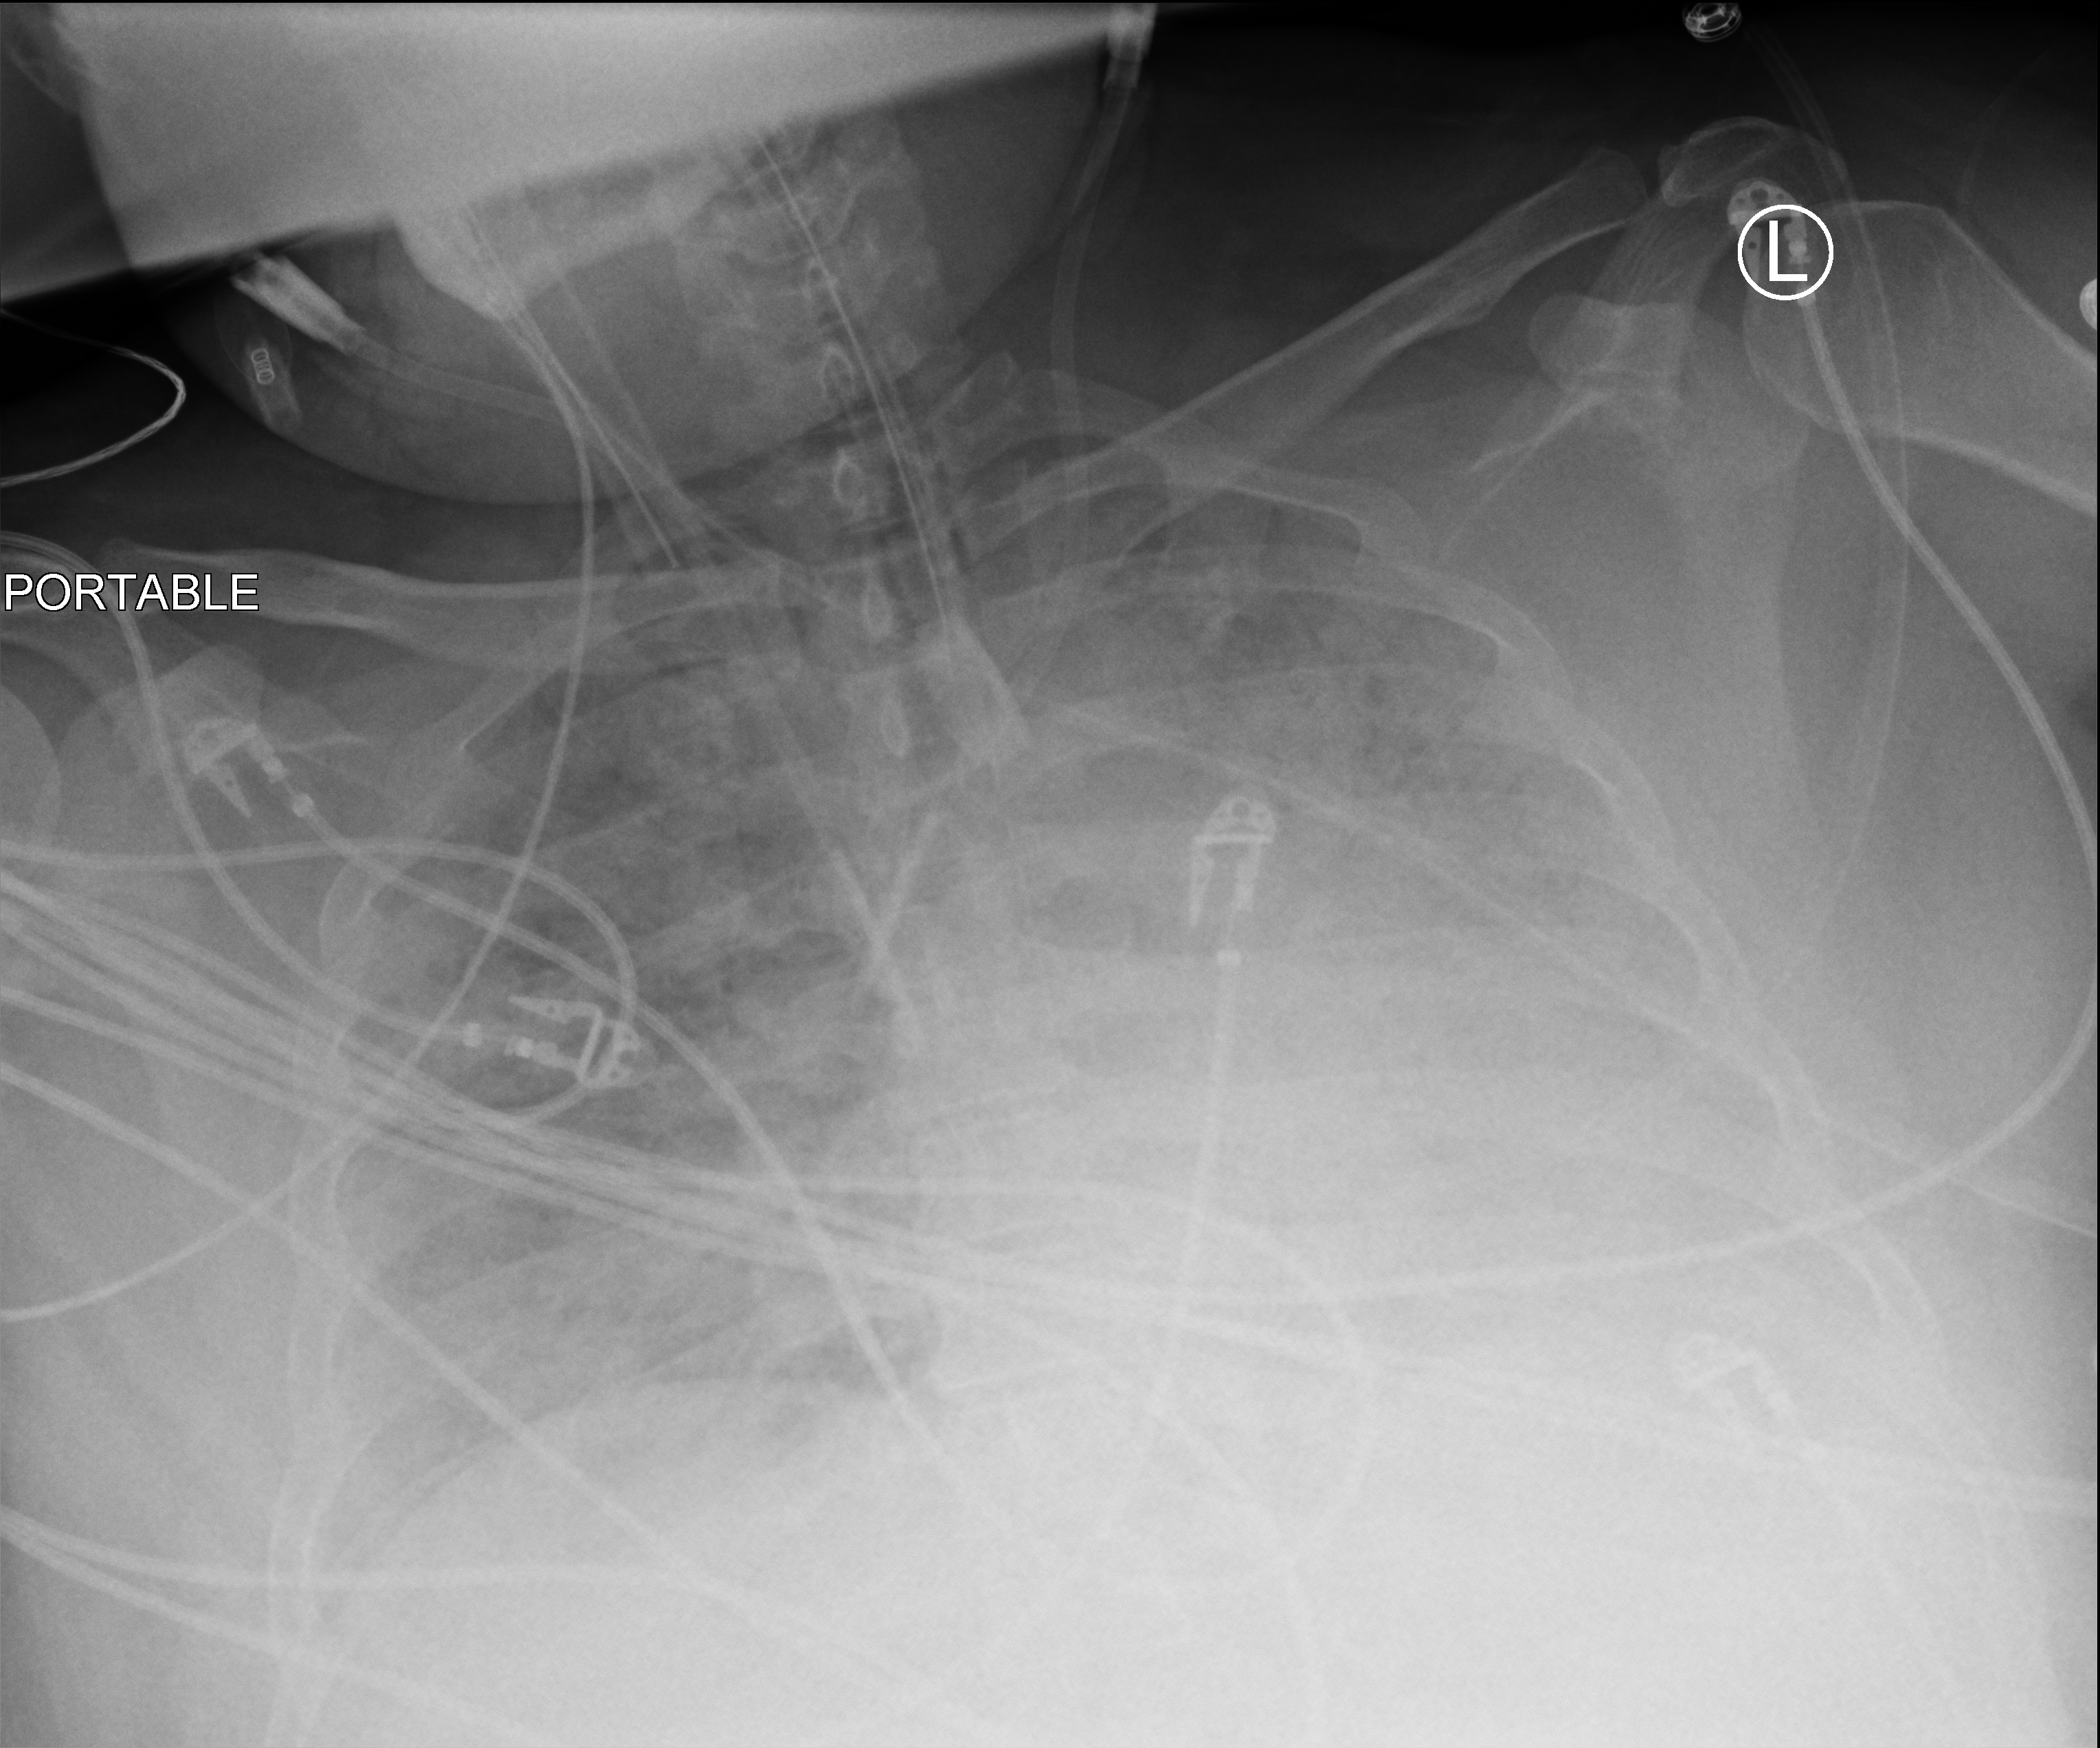
Chest X-ray (portable); anteroposterior (AP) projection. Patient hospitalised with COVID-19, aged 18–59 years.
Hospital-stay facts (about this admission, not read from this image; timing relative to this image not recorded): mechanically ventilated during this hospital stay: yes.